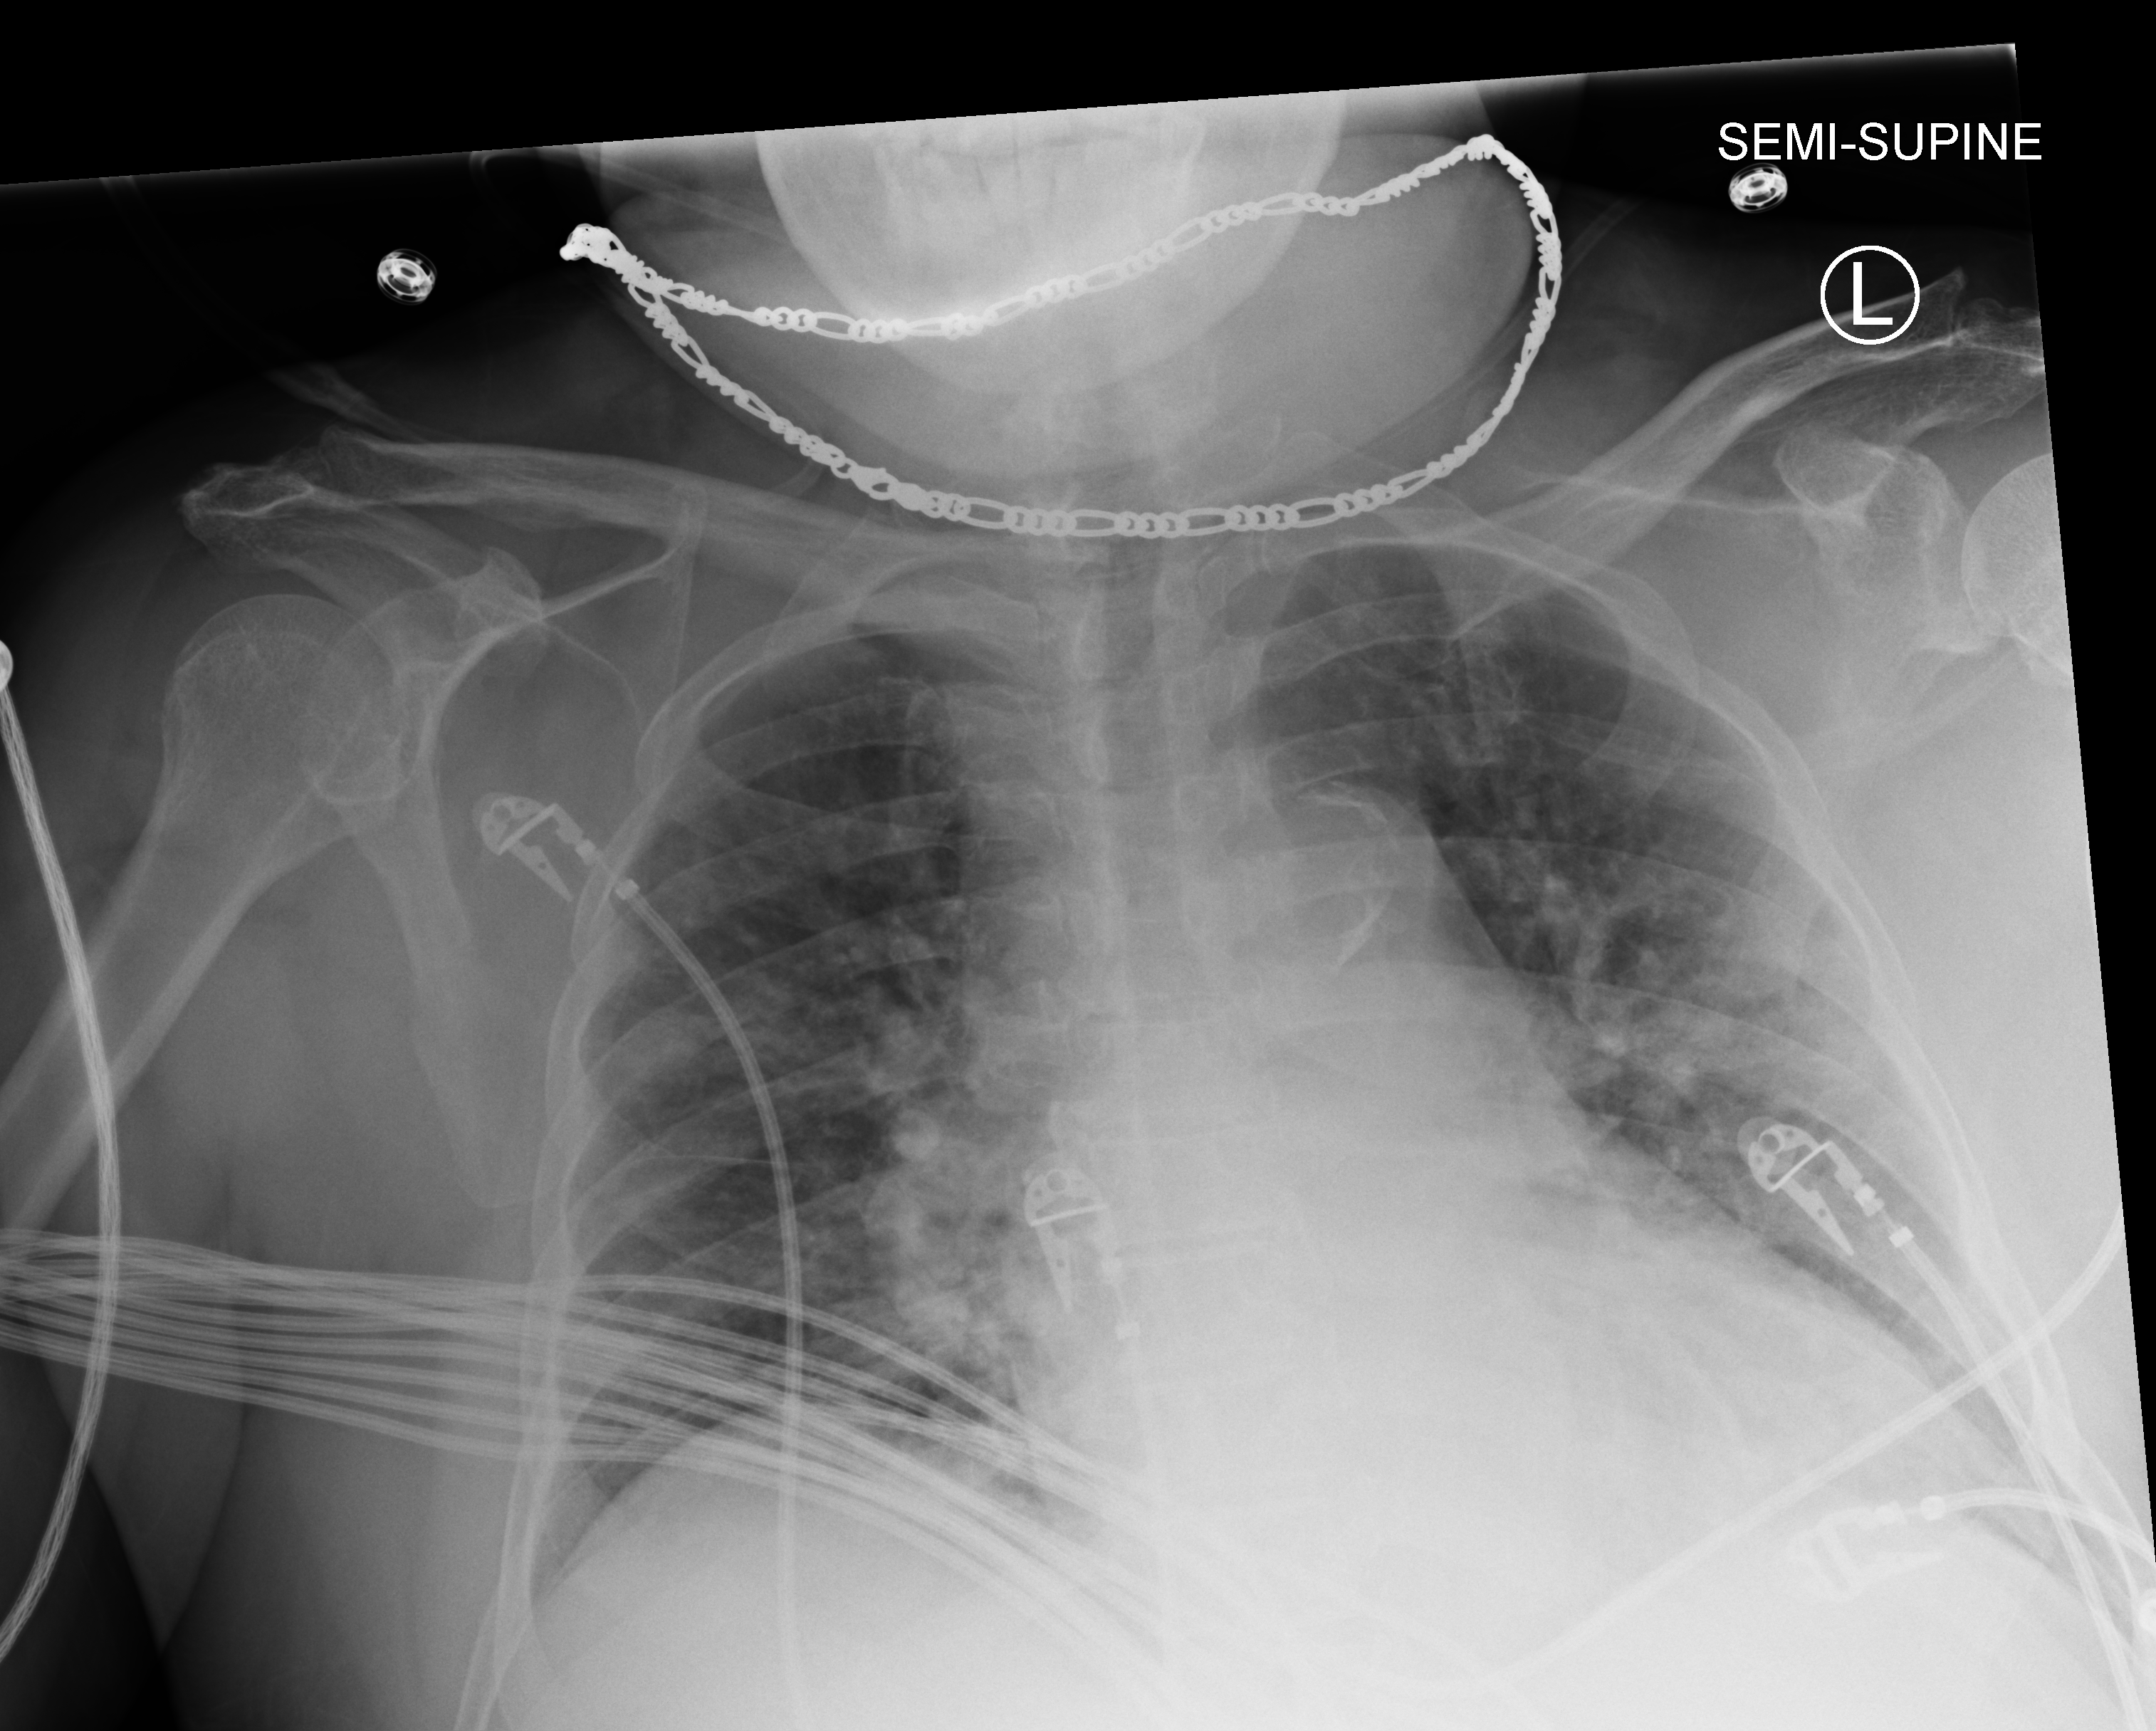
Portable chest radiograph, anteroposterior (AP) projection. Patient hospitalised with COVID-19; male, aged 60–74 years.
Hospital-stay facts (about this admission, not read from this image; timing relative to this image not recorded):
- admitted to intensive care during this hospital stay: yes